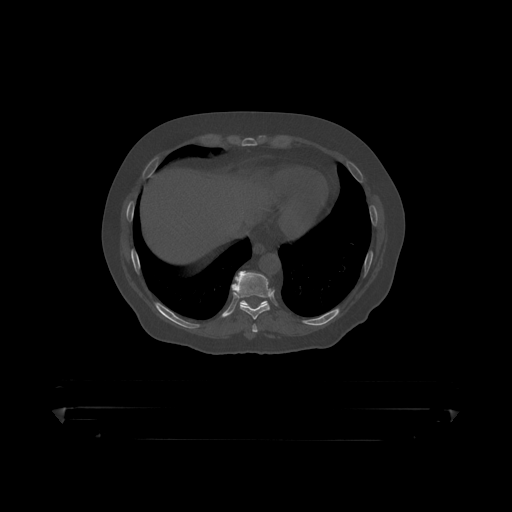
CT including the spine, one axial slice; position 233 of 390 along the scan axis; reconstruction kernel STANDARD; 120 kVp; bone window (W 1800 / L 400 HU); 1.25 mm slice thickness; 512 × 512 image matrix, field of view 650 × 650 mm. Patient: male, 60 years. Case-level facts recorded for this patient, not image findings: primary cancer: prostate.
Annotated regions visible in this slice (semi-automatically segmented with operator editing):
- T10 vertebra: bounding box [x1, y1, x2, y2] px = [240, 301, 267, 307]
- T9 vertebra: [232, 271, 271, 319]